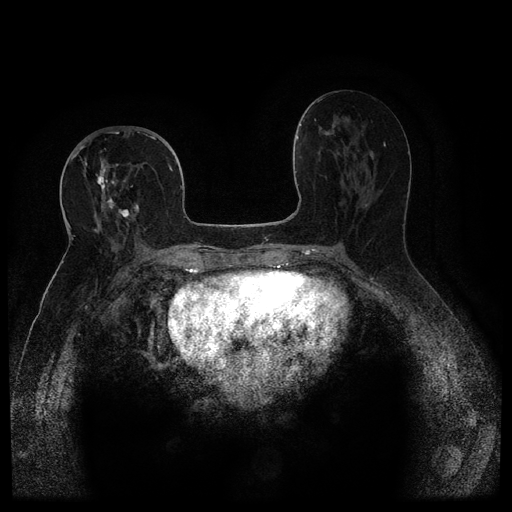
Breast MRI (dynamic contrast-enhanced, multi-phase), one axial slice. Position 53 of 116 along the scan axis. Dynamic contrast-enhanced series, time point 2 of 5 at this slice position (early post-contrast). 1.5 T. TE 2.6 ms, TR 5.4 ms. 512 × 512 image matrix, field of view 340 × 340 mm. Patient: female, 68 years.
Annotated regions visible in this slice (semi-automatic segmentation, software-assisted and operator-edited):
- breast lesion (labelled 'tumour' in the annotation; benign lesions carry a separate 'benign' label): bounding box (x1, y1, x2, y2) in pixels: (94, 157, 116, 214)